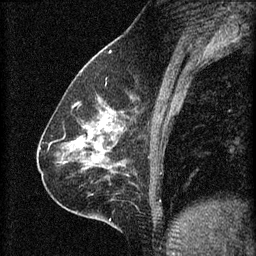
Breast MRI (dynamic contrast-enhanced), one sagittal slice; slice 28 of 60 in the series (ordered by position); 3 images stored at this slice position (order not interpretable as contrast timing); 1.5 T; TE 4.2 ms, TR 8.2 ms; 2 mm slice thickness; 256 × 256 image matrix, field of view 180 × 180 mm. Female patient, age 59 years.
Structures marked on this image (semi-automatic segmentation, software-assisted and operator-edited):
- analysis volume of interest (the breast-tissue region the enhancement analysis was run in; not a lesion): bounding box <61,104,129,161> (left, top, right, bottom; pixels)
- tumour enhancement mask (voxels above the 70 % enhancement threshold inside the analysis volume of interest): <78,112,124,151>